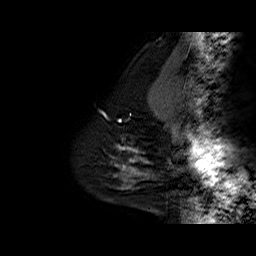
Breast MRI (dynamic contrast-enhanced), one sagittal slice; position 12 of 60 along the scan axis; dynamic contrast-enhanced series, time point 2 of 6 at this slice position (early post-contrast); 1.5 T; TE 6.3 ms, TR 32.5 ms; 256 × 256 image matrix, field of view 200 × 200 mm. Female patient. Case-level facts recorded for this patient, not image findings: setting: breast cancer imaged before/during neoadjuvant chemotherapy; receptor status: triple-negative.
Outlined on this slice (semi-automatically segmented with operator editing):
- analysis volume of interest (the breast-tissue region the enhancement analysis was run in; not a lesion): box from (x=110, y=145) to (x=148, y=177) px
- tumour enhancement mask (voxels above the 100 % enhancement threshold inside the analysis volume of interest): (x=118, y=146)–(x=147, y=171)